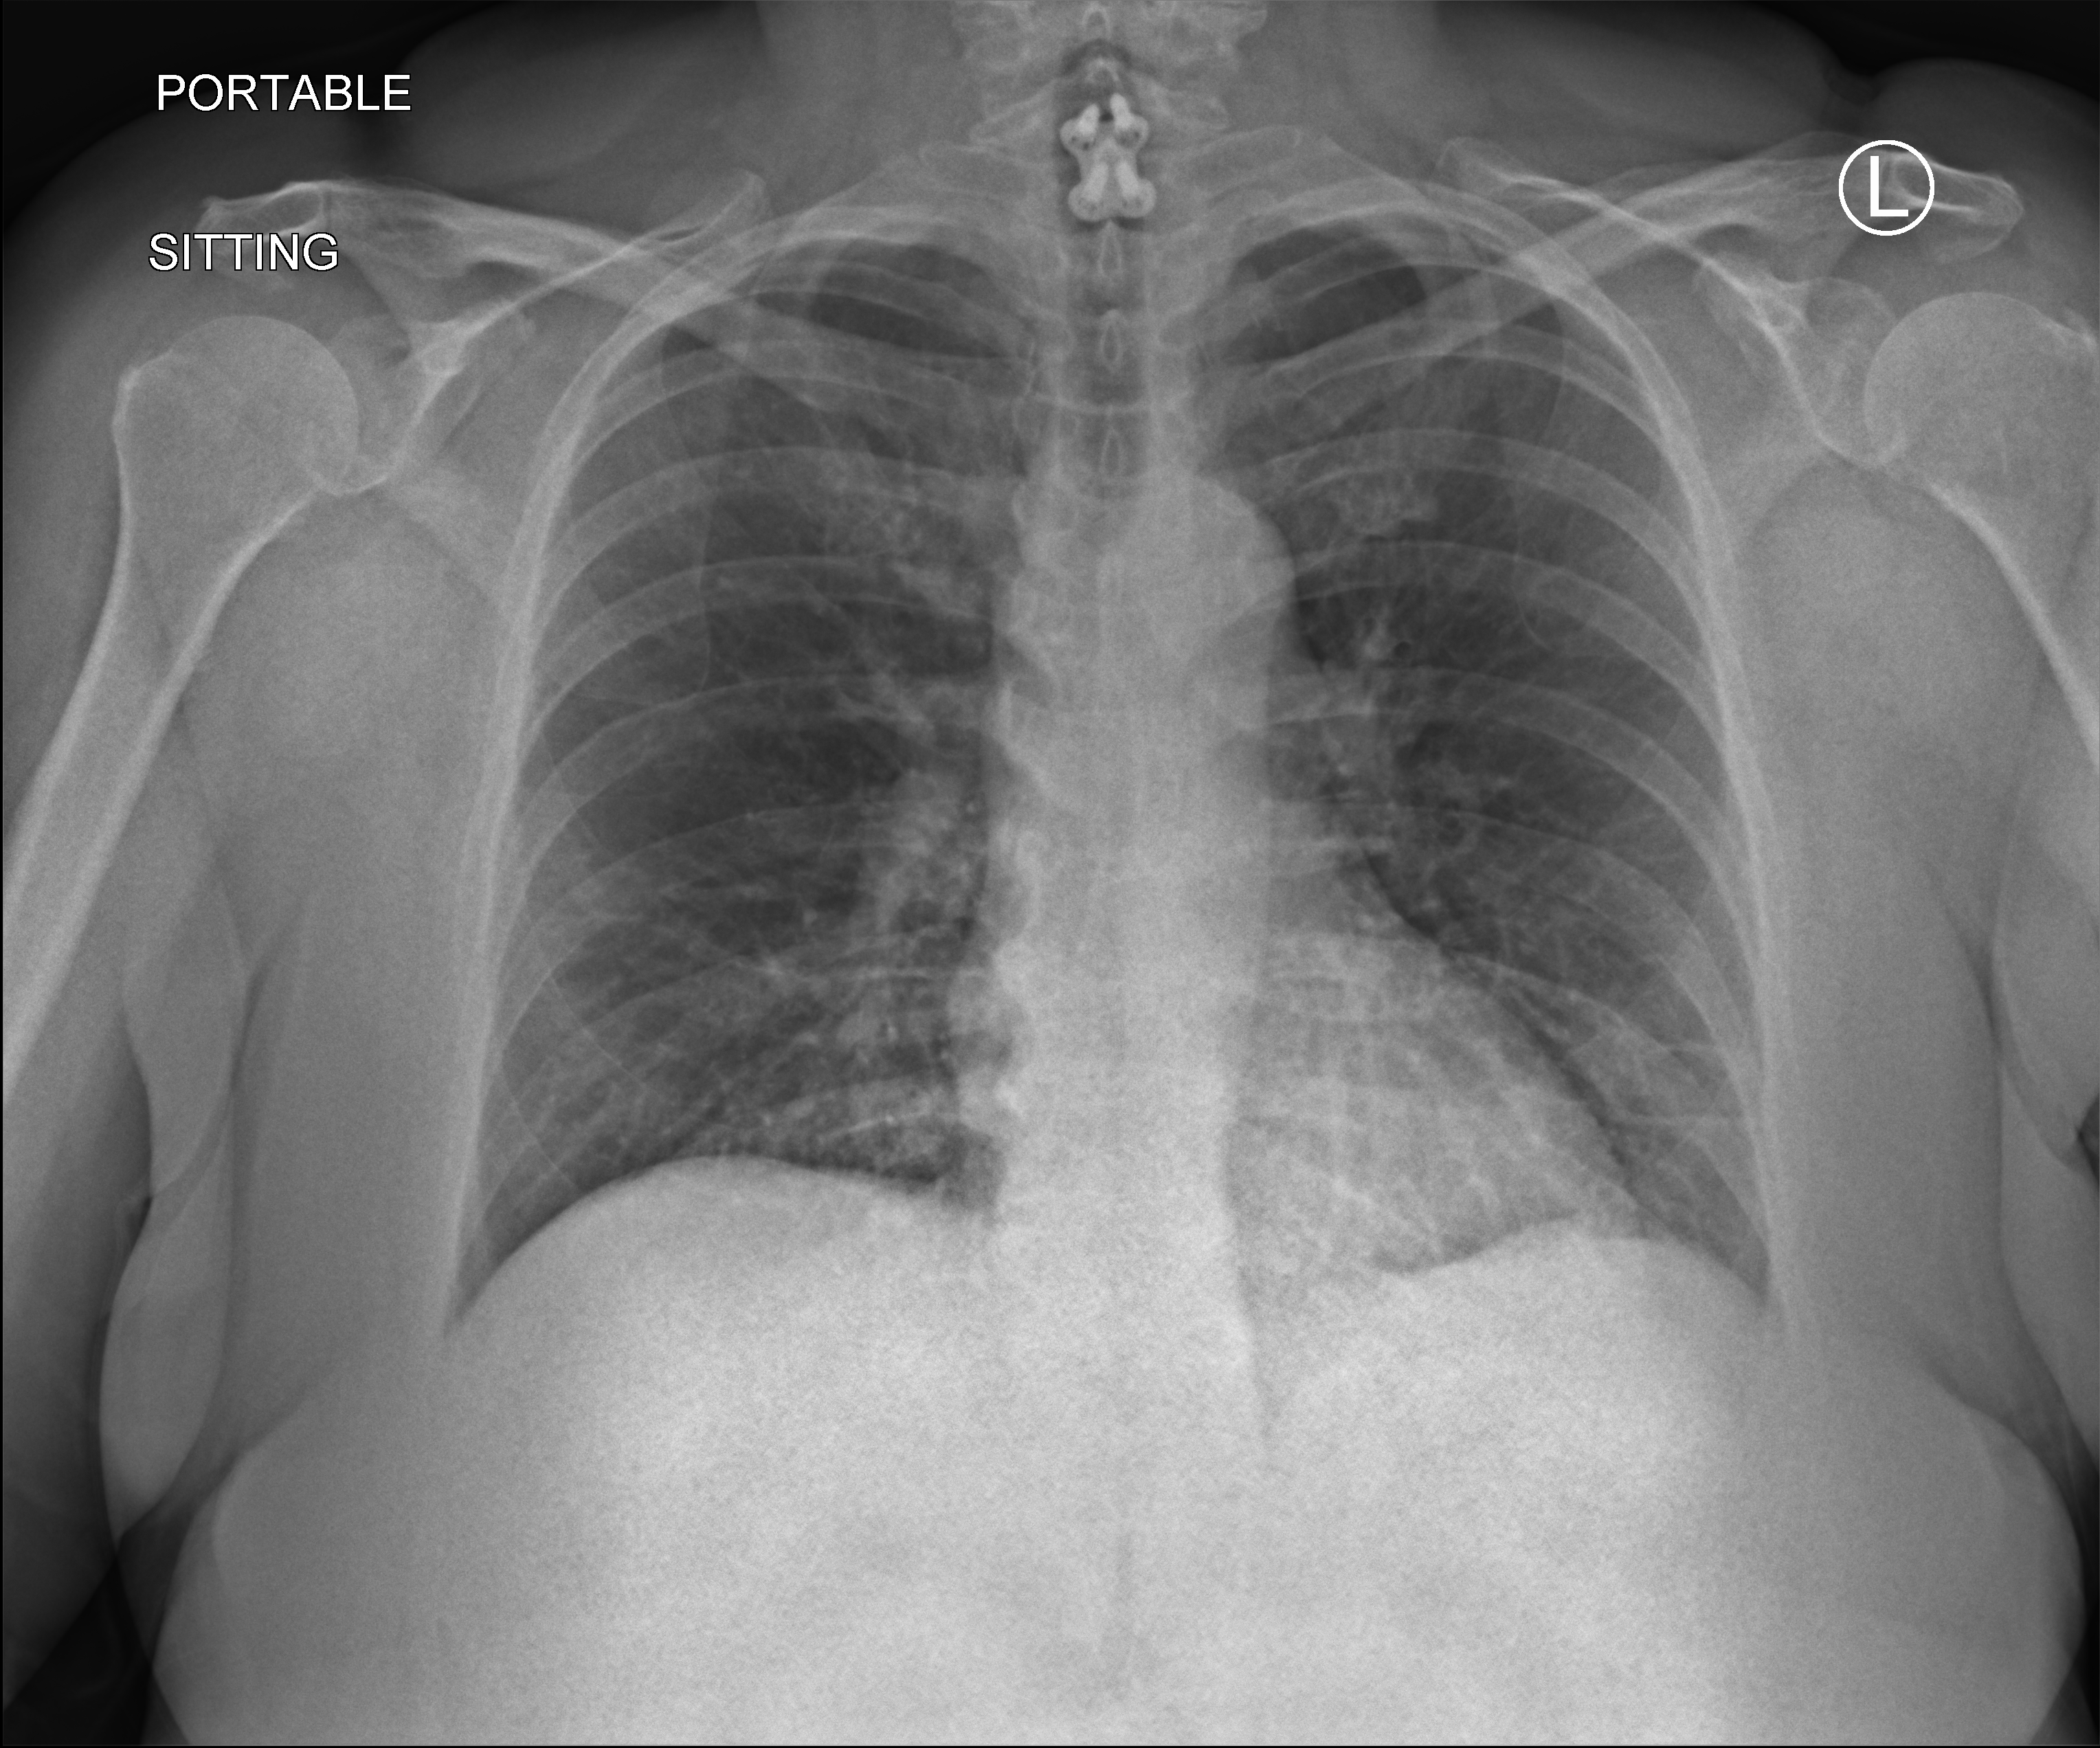
Portable chest radiograph; anteroposterior (AP) projection. Female patient hospitalised with COVID-19, age 18–59 years.
Admission-level facts for this patient (not findings on this image; timing relative to this image not recorded):
- smoking status (admission record): former
- diabetes (admission record): no